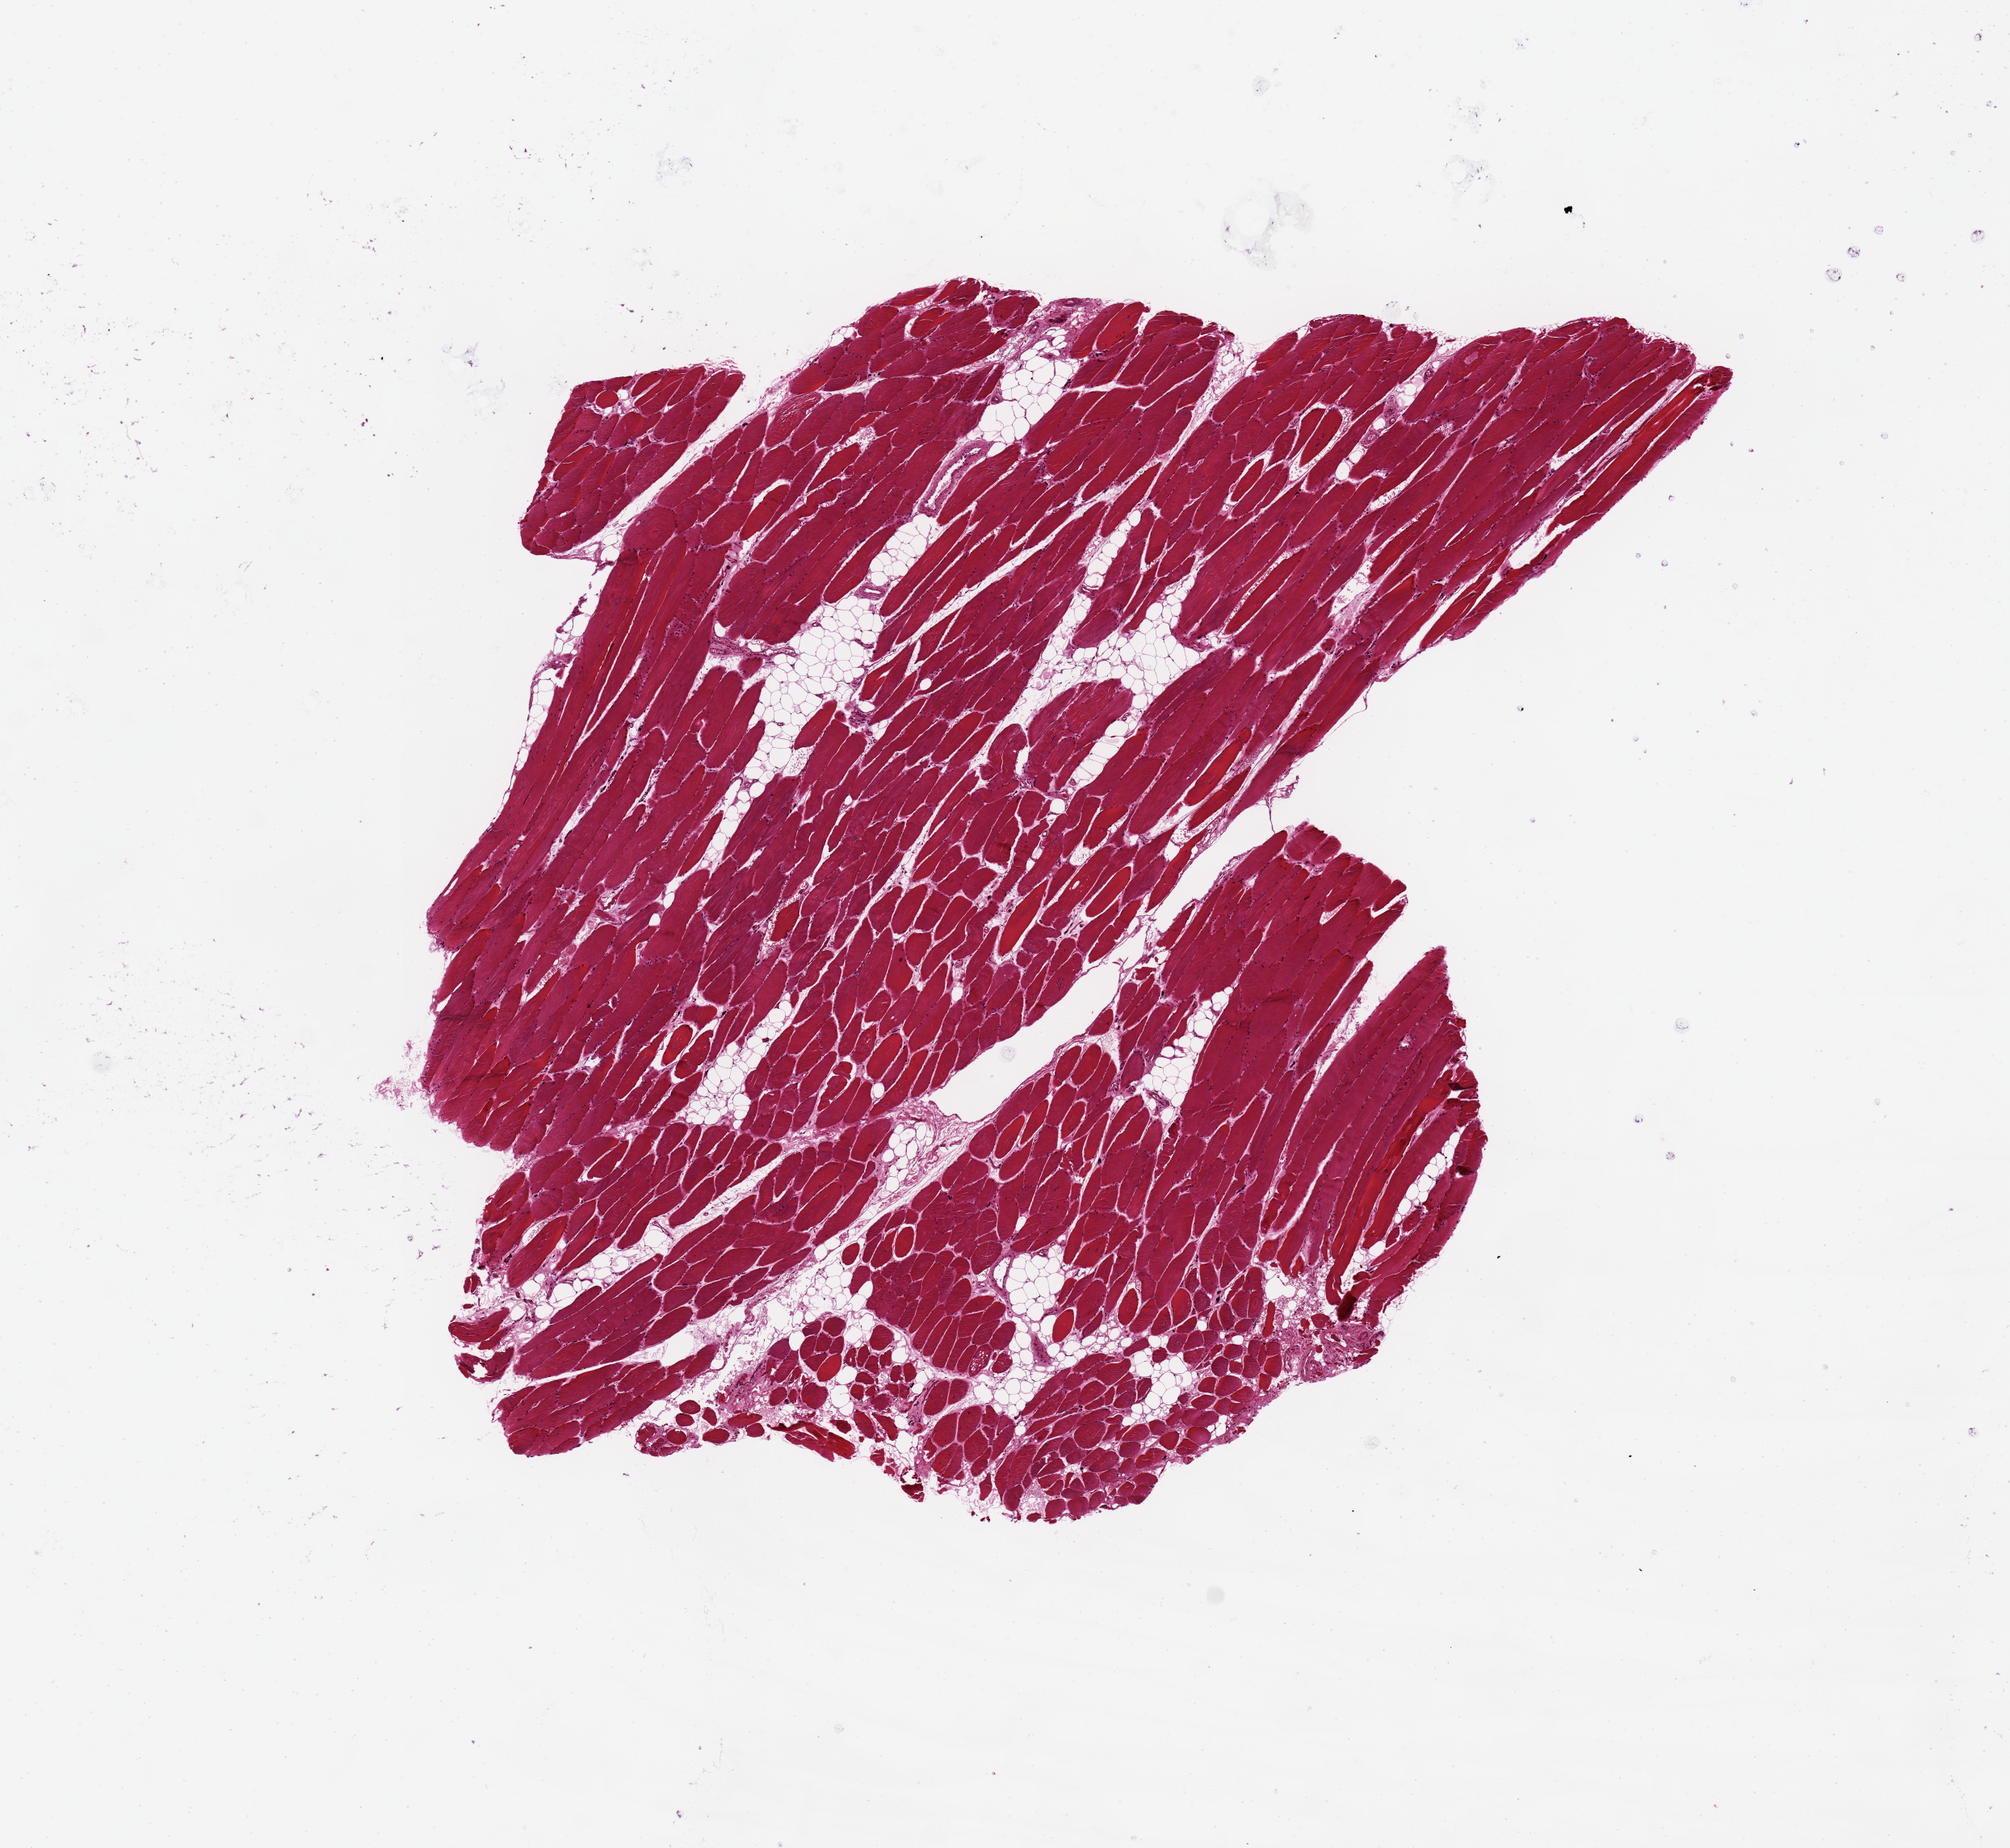
Whole-slide image, hematoxylin and eosin (H&E) stain, brightfield — whole scanned area (about 9.8 x 9.0 mm) shown as a low-resolution overview, PAXgene-fixed paraffin-embedded (PFPE) section, section of skeletal muscle (target tissue), tissue donor sample. Donor sex: male.
* pathologist's review note for this sample: ~10% intramuscular fat